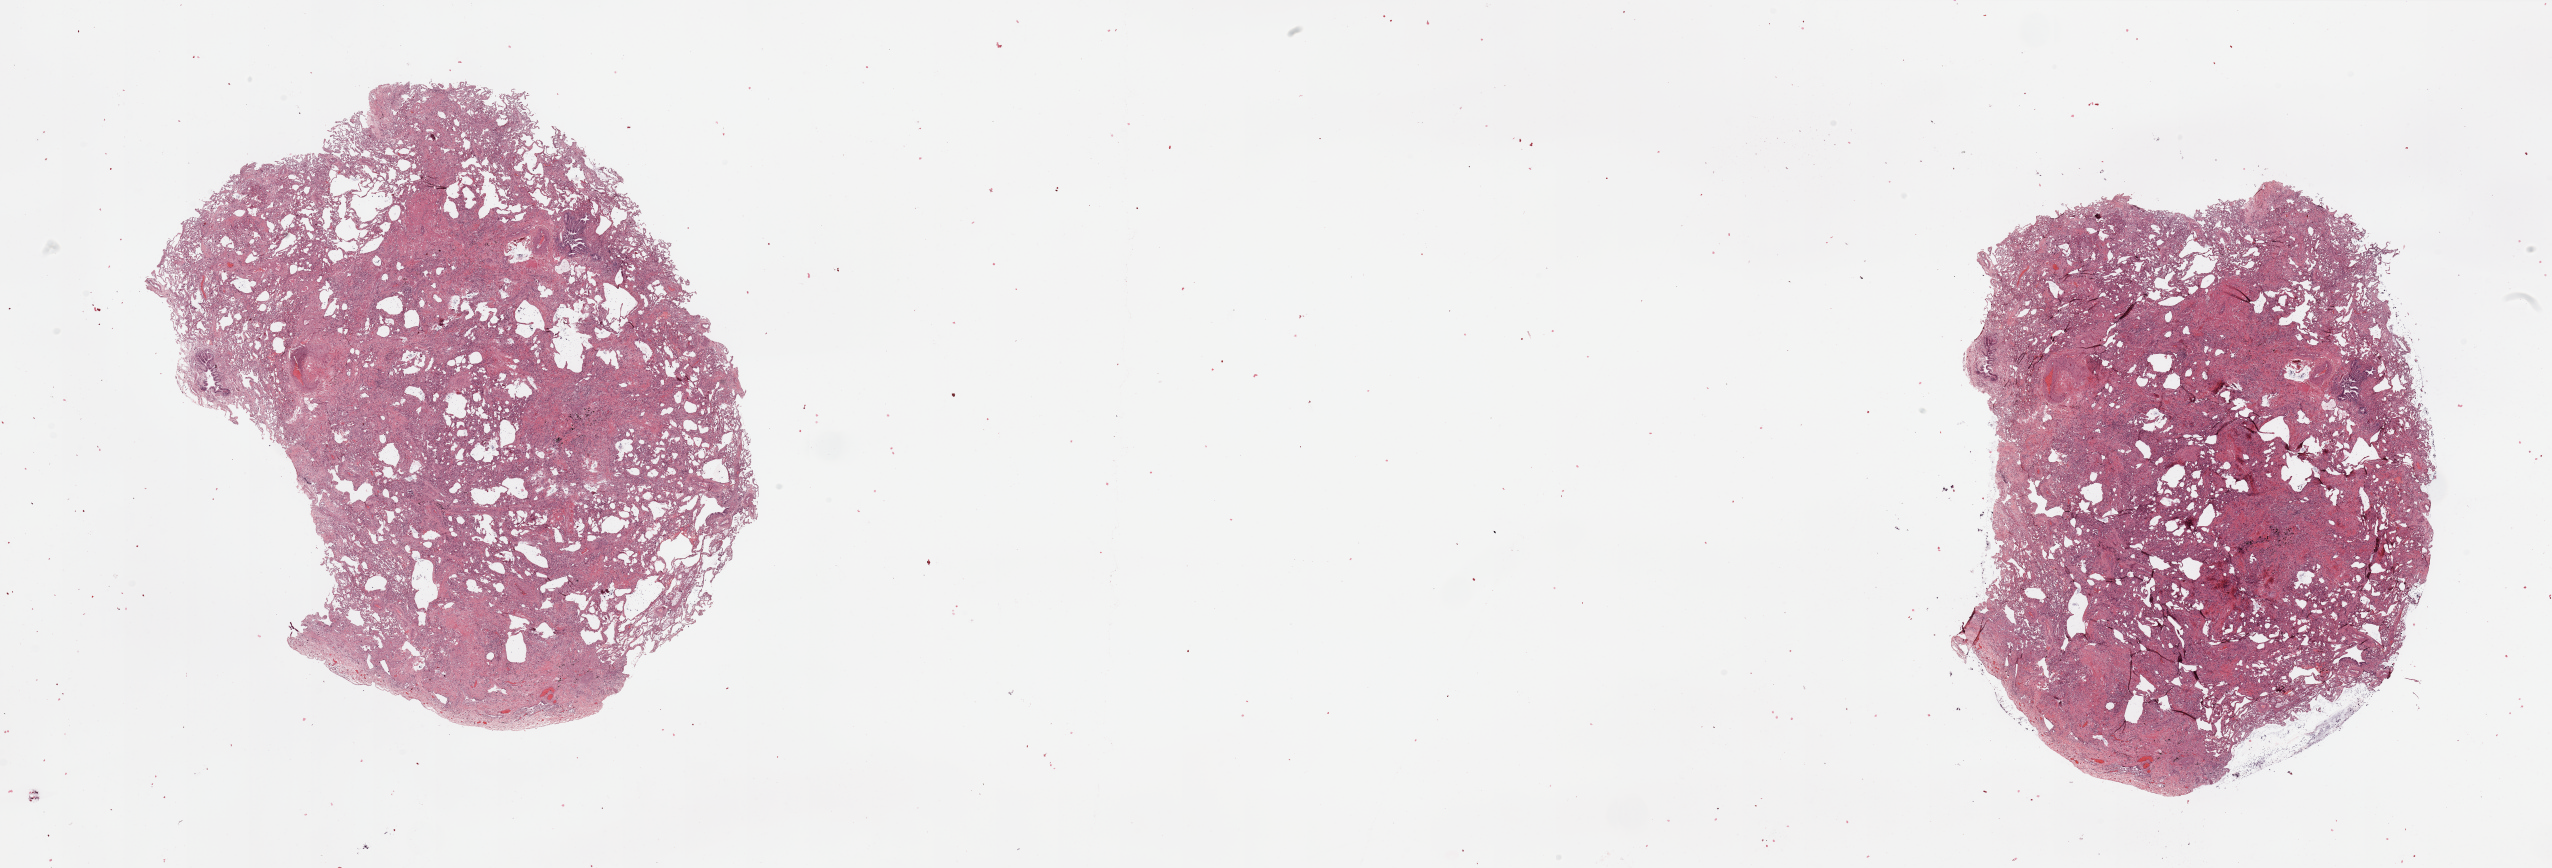
Whole-slide histology image, H&E-stained — whole scanned area (about 40.4 x 13.7 mm) shown as a low-resolution overview, normal (non-tumour) tissue sample, lung. 68-year-old male patient.
This section: normal (non-tumour) tissue from the same patient. Patient diagnosis (cohort enrolment): squamous cell carcinoma (lung).